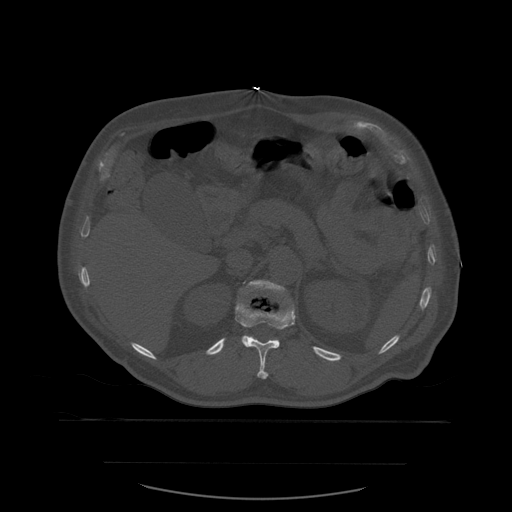
CT including the spine, one axial slice. Slice 266 of 590 in the series (ordered by position). Bone window (W 1800 / L 400 HU). 1.25 mm slice thickness. 512 × 512 image matrix. Patient age 71 years. Case-level facts recorded for this patient, not image findings: primary cancer: lung; vertebrae with lytic lesions (as recorded): T1, T2, L5, S1.
Outlined on this slice (semi-automatically segmented with operator editing):
- L1 vertebra: box from (x=242, y=280) to (x=295, y=339) px
- T12 vertebra: (x=235, y=301)–(x=296, y=380)